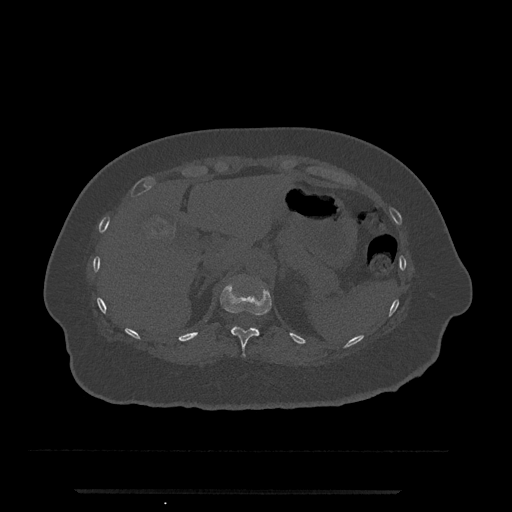
CT including the spine, one axial slice. Slice 216 of 797 in the series (ordered by position). 120 kVp. Bone window (W 1800 / L 400 HU). 512 × 512 image matrix, field of view 440 × 440 mm. Patient: female, 51 years. From the clinical record (not read from this slice): primary cancer: neuro; vertebrae with lytic lesions (as recorded): T8.
Outlined on this slice (semi-automatic segmentation, software-assisted and operator-edited):
- T11 vertebra: bounding box (x1, y1, x2, y2) in pixels: (220, 285, 272, 357)